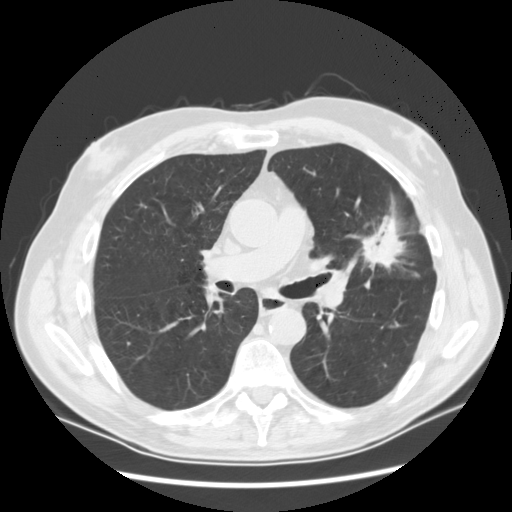
Low-dose screening chest CT, axial slice; first (baseline) screen; lung window (W 1500 / L -600 HU); slice 58 of 132 in the series; 512 × 512 image matrix. Male, age 65 years at enrolment.
Expert reader's lesion annotation, box from (x=349, y=215) to (x=415, y=283) px. Reader record for this screening exam (exam-level; its link to the box is not recorded): non-calcified nodule or mass ≥4 mm, left upper lobe, 37 × 27 mm, spiculated (stellate) margins, soft tissue attenuation. Participant outcome: lung cancer diagnosed 56 days after this screen — non-small cell carcinoma, poorly differentiated (G3), stage IA (AJCC 6th edition).